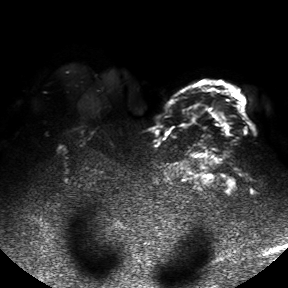
Breast MRI, one axial slice; slice 36 of 50 in the series (ordered by position); diffusion-weighted series; image 2 of 4 stored at this slice position (different b-values; order by instance number); 1.5 T; 288 × 288 image matrix. Female patient.
Annotated regions visible in this slice (expert manual segmentation):
- tumour on diffusion-weighted imaging: bounding box [x1, y1, x2, y2] px = [212, 112, 229, 136]